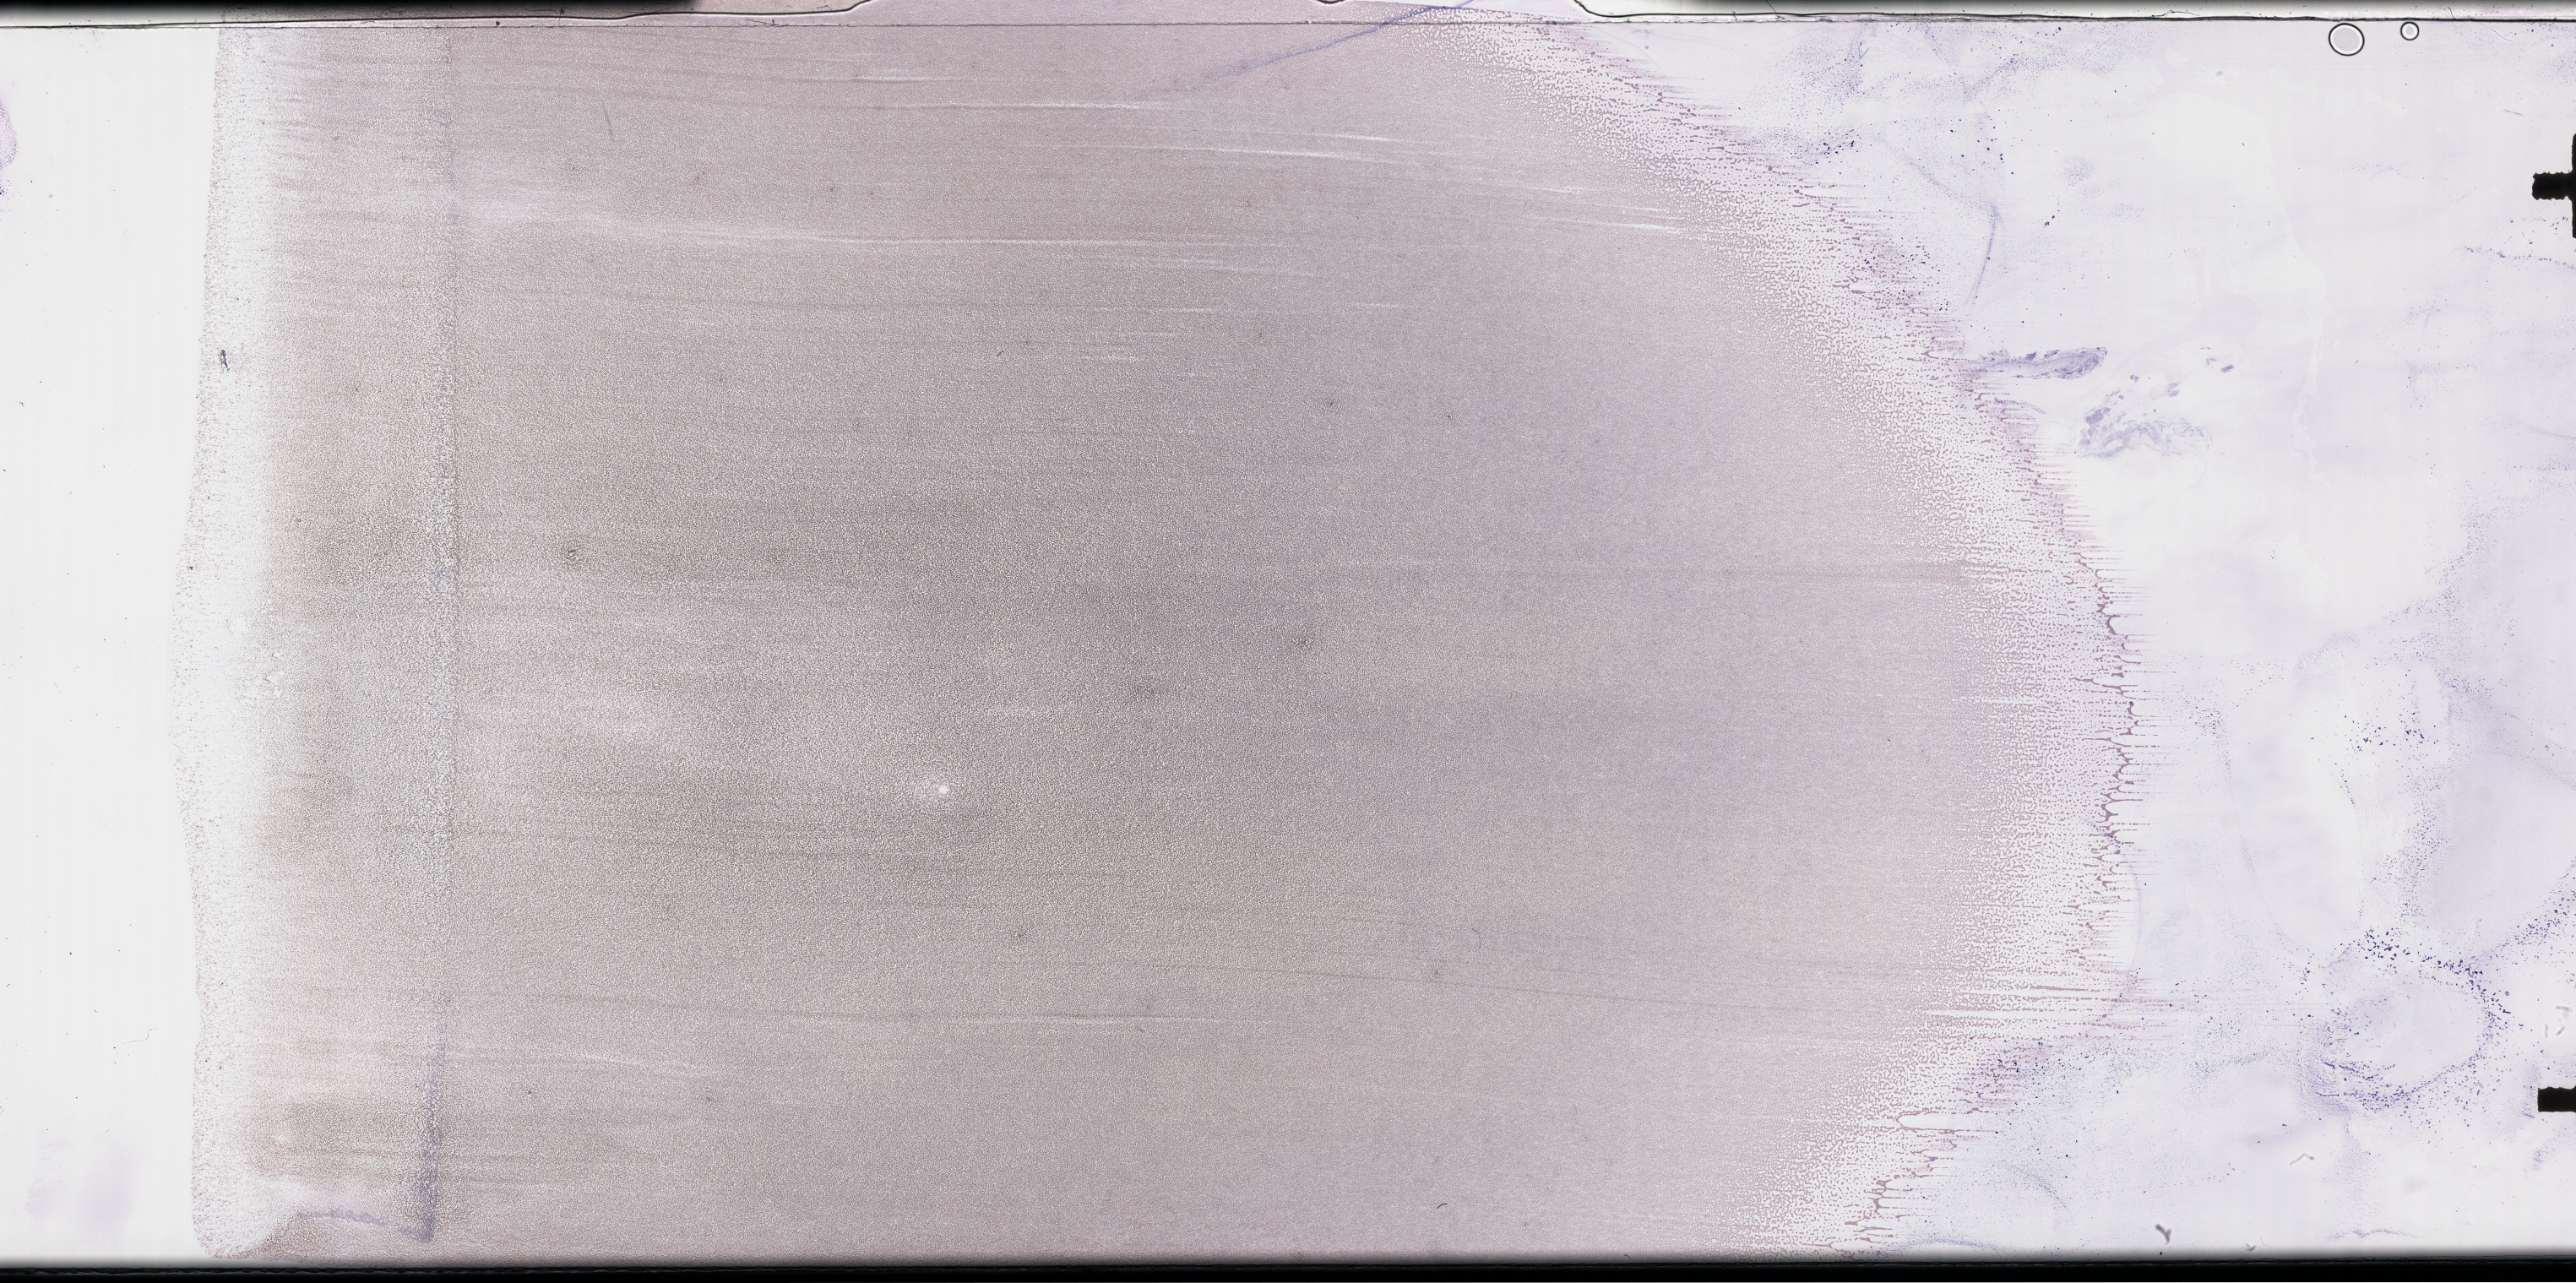
Whole-slide image of a whole blood smear, Wright-Giemsa stain, whole scanned area (about 49.3 x 24.5 mm) shown as a low-resolution overview. Smear from an EDTA sample. Specimen time point: collected post-treatment, no progression. Patient sex: female.
From a patient with: Acute Myeloid Leukemia Not Otherwise Specified.